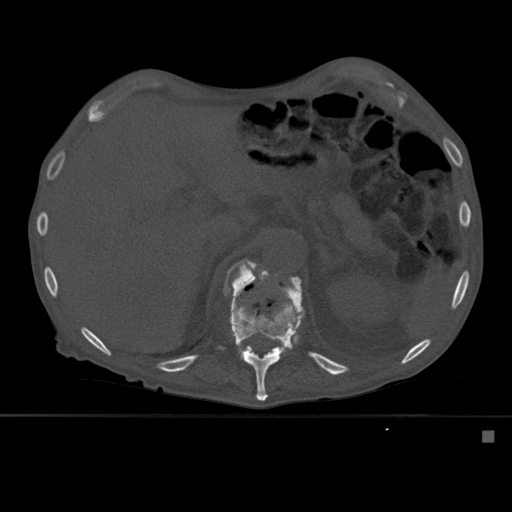
CT including the spine, one axial slice; position 273 of 527 along the scan axis; bone window (W 1800 / L 400 HU); 1.5 mm slice thickness; 512 × 512 image matrix. Male patient, age 78 years. From the clinical record (not read from this slice): primary cancer: prostate.
Structures marked on this image (semi-automatically segmented with operator editing):
- L1 vertebra: bounding box <250,262,259,269> (left, top, right, bottom; pixels)
- T12 vertebra: <224,259,305,401>